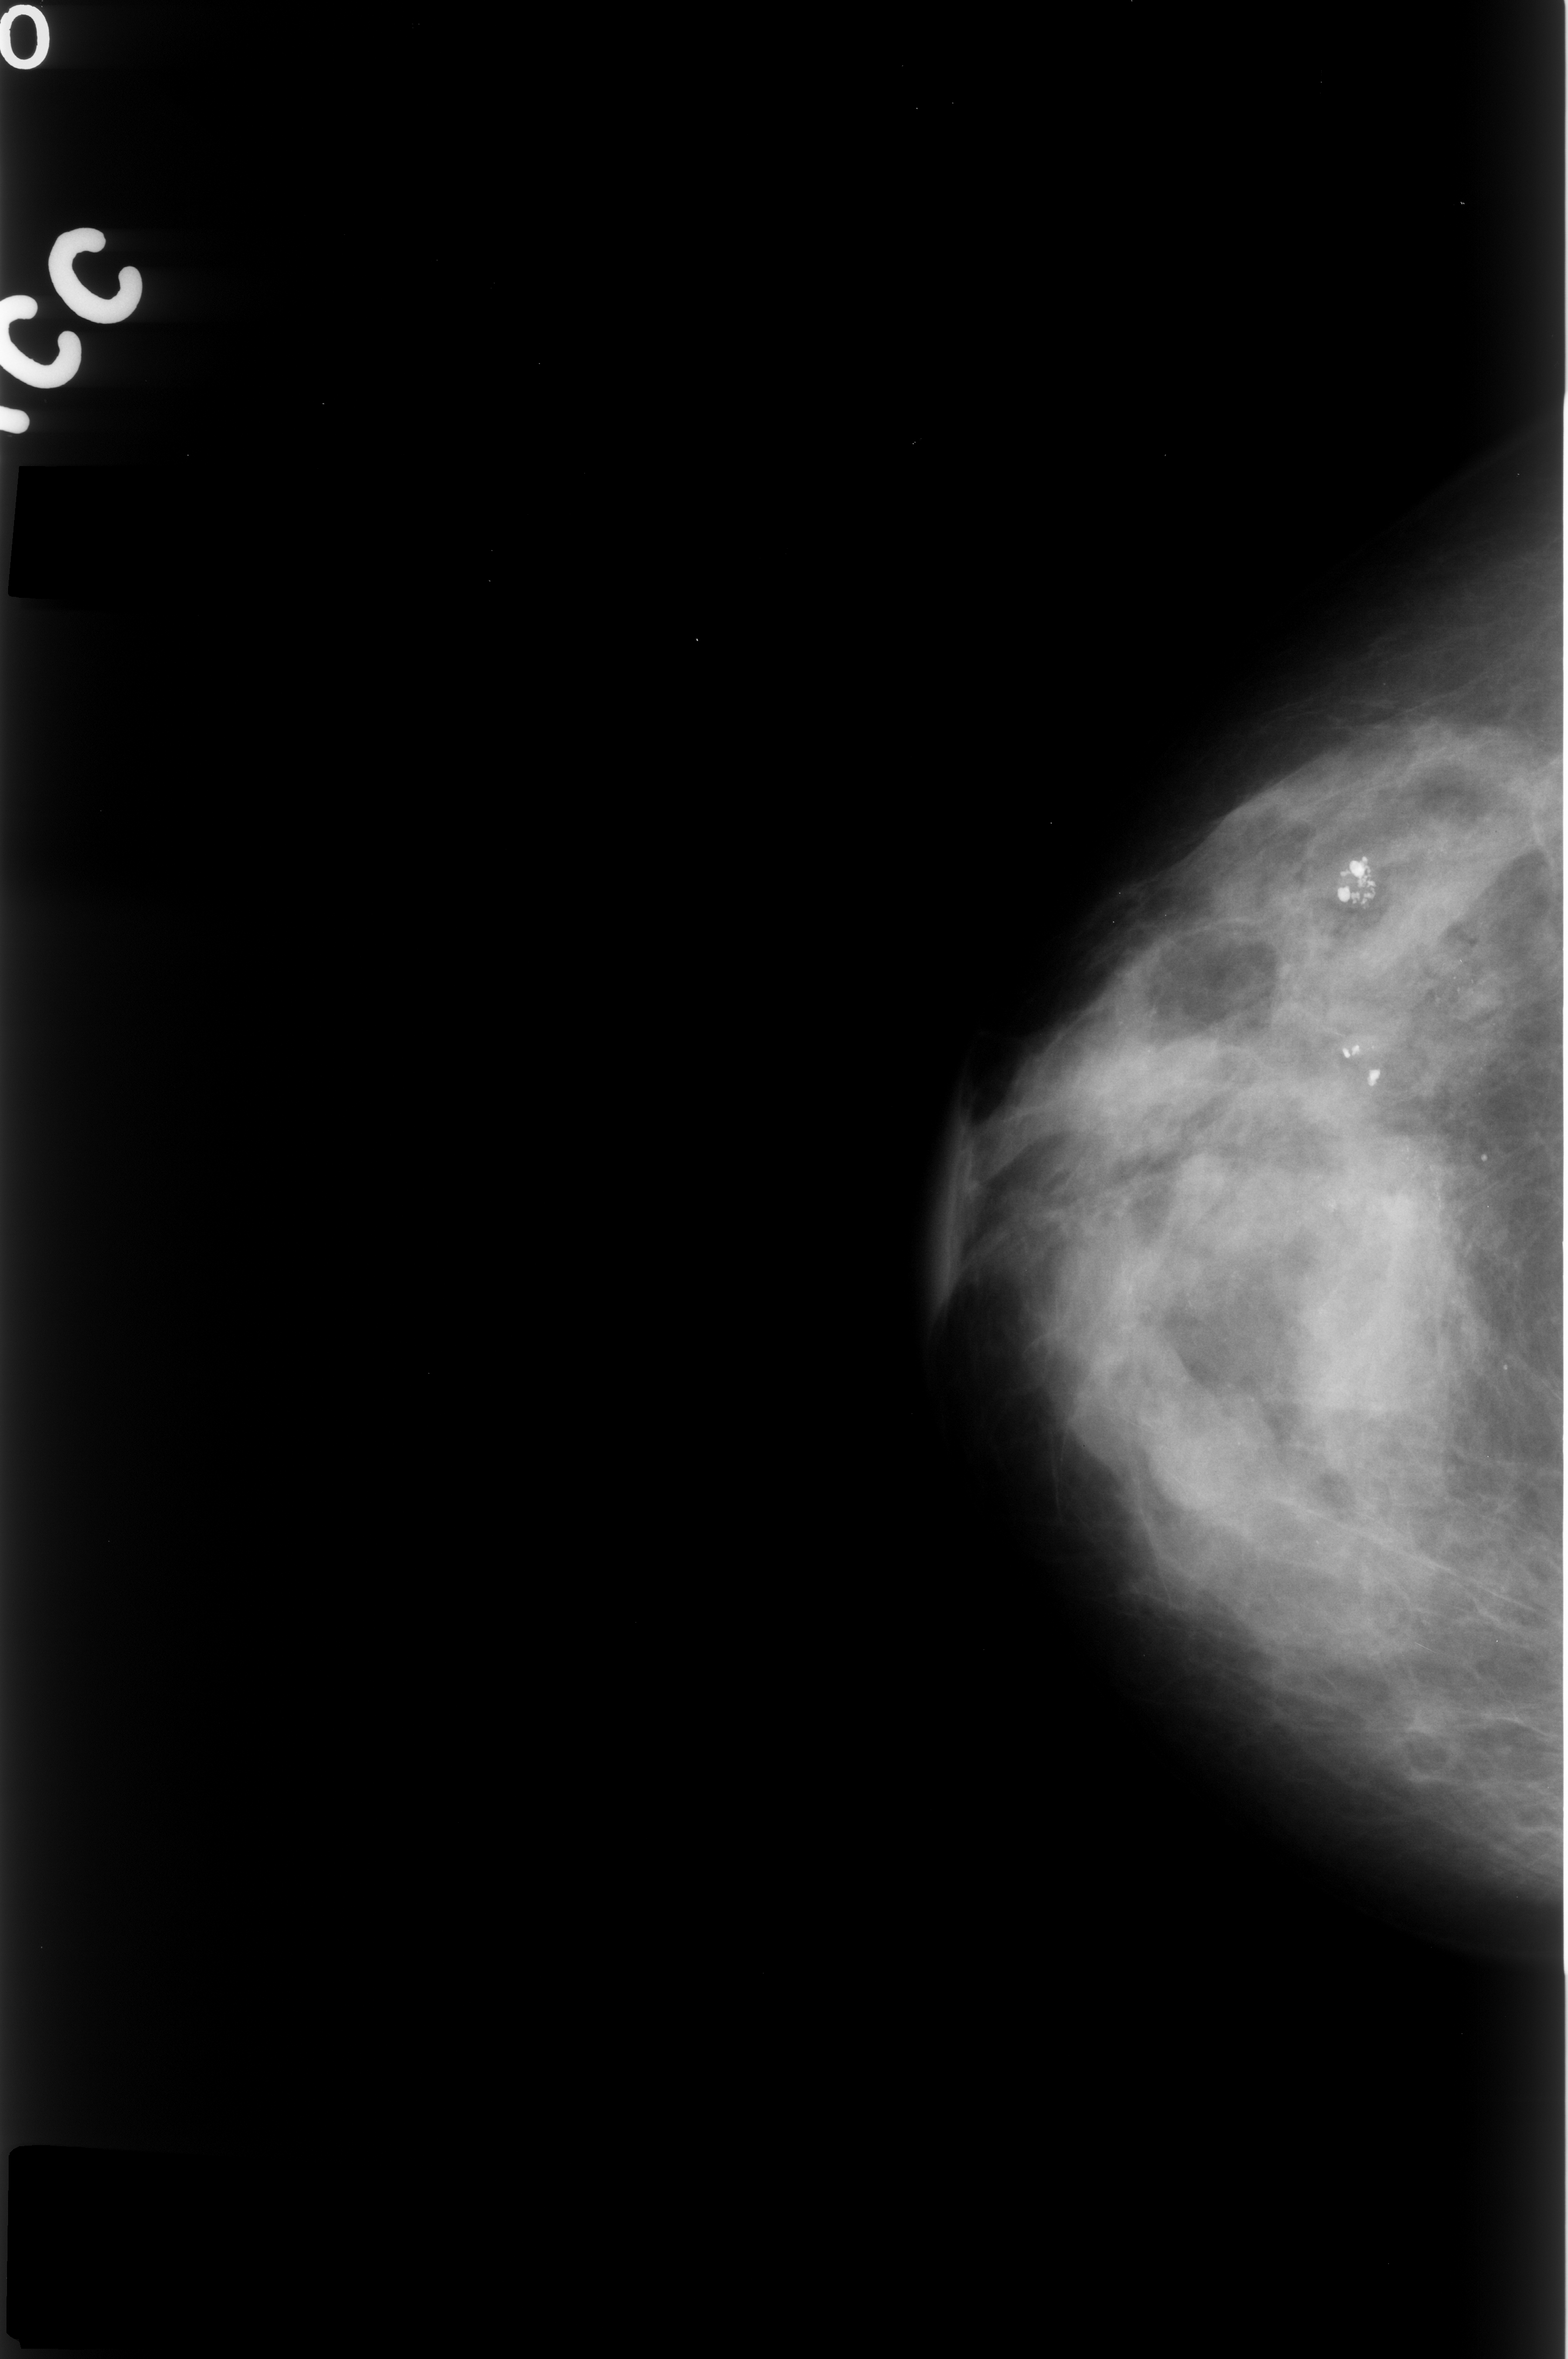
Mammogram (digitized film); right breast; CC view; 1568 × 2359 image matrix.
Expert-marked regions of interest on this film, with their recorded descriptors:
- calcifications, morphology amorphous, distribution clustered; BI-RADS assessment category 4; subtlety rating 2 on a 1 (subtle) to 5 (obvious) scale; pathology result (as recorded, not read from the image): benign: bounding box [x1, y1, x2, y2] px = [1287, 1097, 1500, 1232]